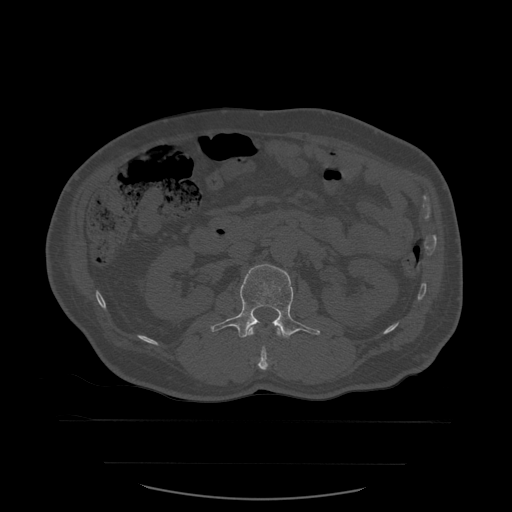
CT including the spine, one axial slice. Position 225 of 590 along the scan axis. Bone window (W 1800 / L 400 HU). 512 × 512 image matrix. Patient age 71 years. From the clinical record (not read from this slice): primary cancer: lung.
Annotated regions visible in this slice (semi-automatically segmented with operator editing):
- L1 vertebra: box from (x=248, y=328) to (x=281, y=371) px
- L2 vertebra: (x=211, y=264)–(x=321, y=339)